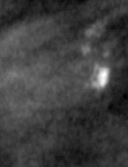
Region of interest cut from a scanned film mammogram (one marked finding), left breast, MLO view, BI-RADS breast density category 2 (scale 1–4).
- Marked abnormality: calcifications, morphology pleomorphic, distribution linear; BI-RADS assessment category 4; subtlety rating 1 on a 1 (subtle) to 5 (obvious) scale; pathology (as recorded): malignant.